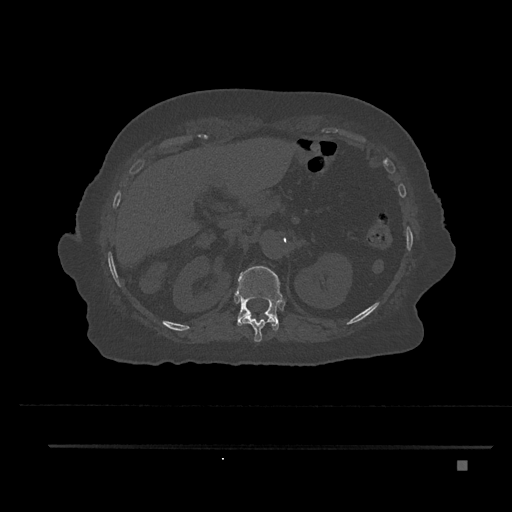
CT including the spine, one axial slice. Slice 283 of 797 in the series (ordered by position). Reconstruction kernel Br40s/3. Bone window (W 1800 / L 400 HU). 0.5 mm slice thickness. 512 × 512 image matrix, field of view 437 × 437 mm. Female patient, age 76 years. Case-level facts recorded for this patient, not image findings: primary cancer: lung.
Annotated regions visible in this slice (semi-automatically segmented with operator editing):
- T11 vertebra: box from (x=240, y=314) to (x=275, y=342) px
- T12 vertebra: (x=237, y=266)–(x=283, y=332)